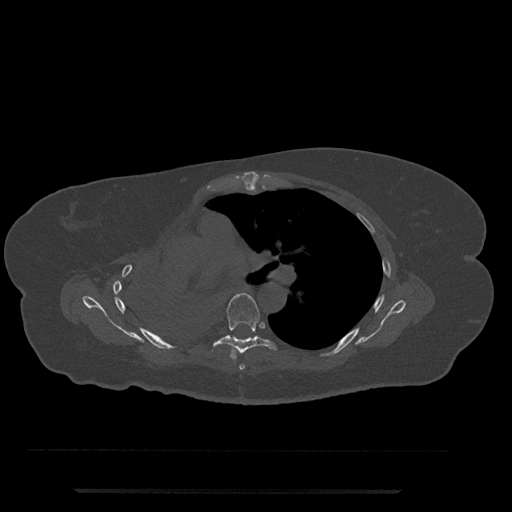
CT including the spine, one axial slice. Slice 498 of 797 in the series (ordered by position). Reconstruction kernel Br40s/3. 120 kVp. Bone window (W 1800 / L 400 HU). 0.5 mm slice thickness. 512 × 512 image matrix, field of view 440 × 440 mm. Female patient, age 51 years. From the clinical record (not read from this slice): primary cancer: neuro.
Outlined on this slice (semi-automatic segmentation, software-assisted and operator-edited):
- T5 vertebra: bounding box (x1, y1, x2, y2) in pixels: (239, 364, 245, 370)
- T6 vertebra: (211, 293, 278, 359)